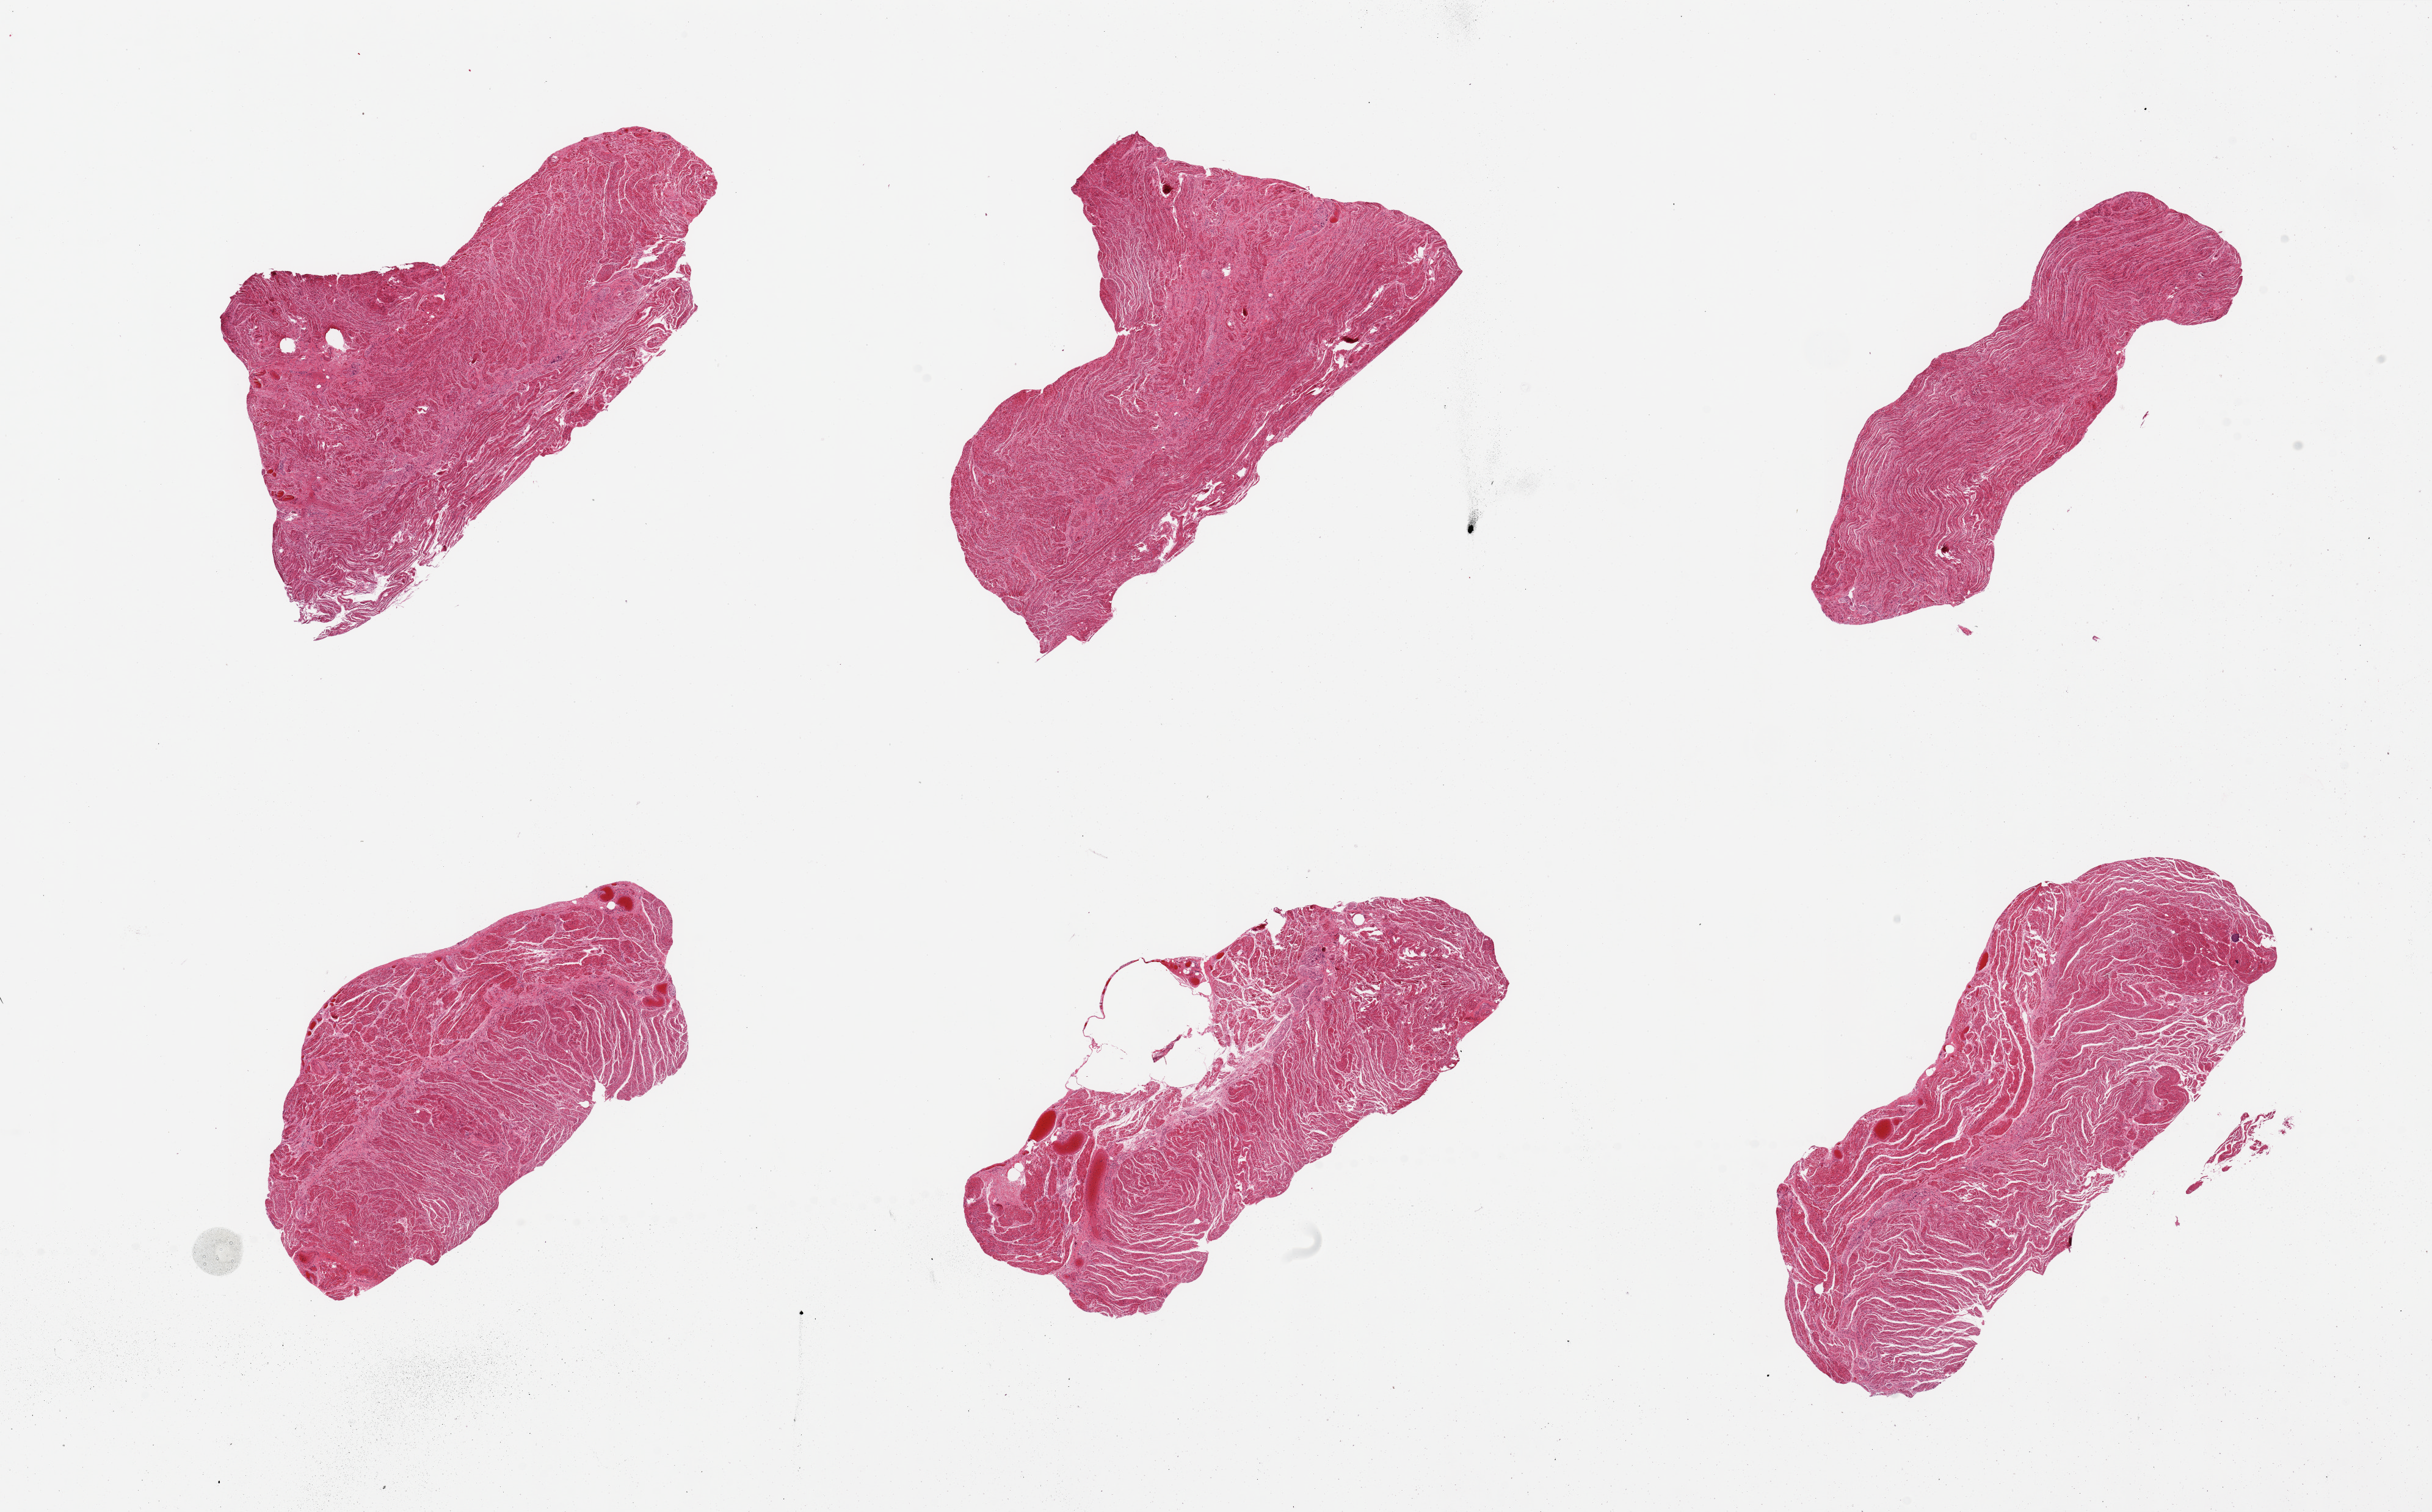
Hematoxylin and eosin (H&E) whole-slide image, brightfield — low-resolution overview of the scanned area, about 31.5 x 19.6 mm (acquisition: 20x scan); PAXgene-fixed, paraffin-embedded tissue; target tissue: gastroesophageal junction; donor tissue sample.
- reviewer comment on this tissue sample: 6 pieces, all muscularis, good specimens